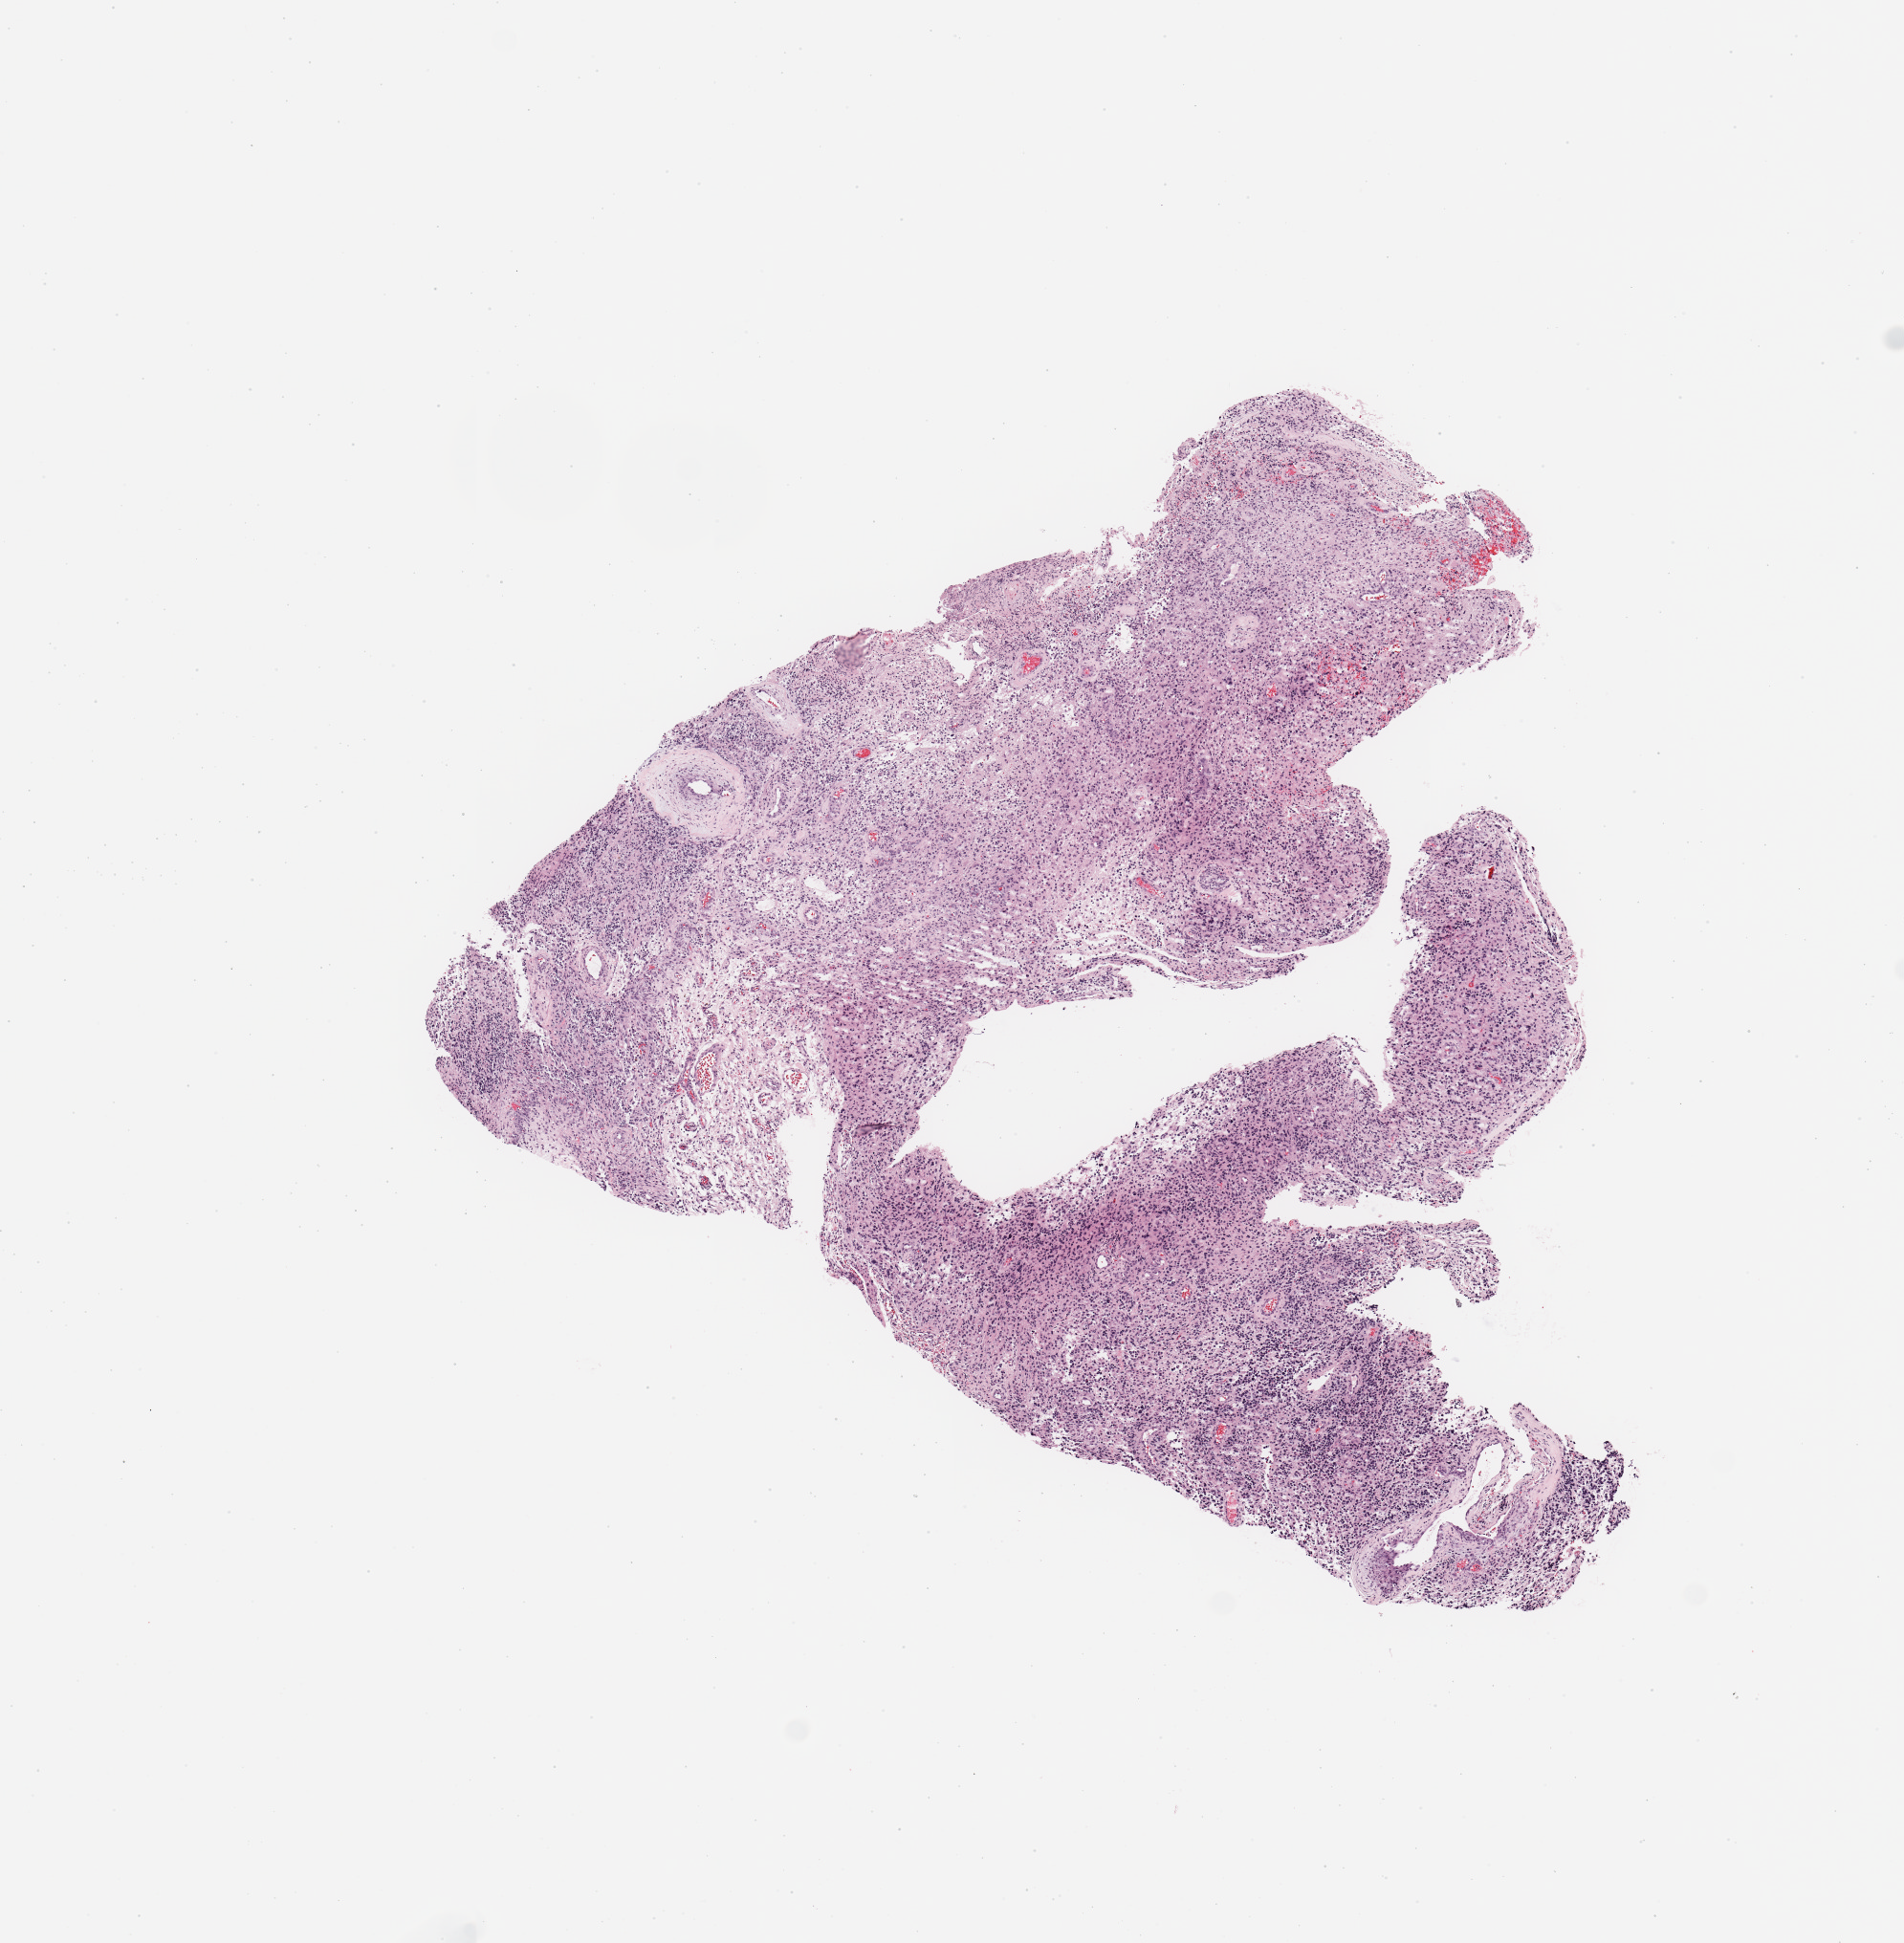
Whole-slide histology image, H&E, low-resolution overview of the scanned area, about 7.9 x 8.0 mm (acquisition: 20x scan). Brain, tumour tissue. 58-year-old female patient.
Histologic diagnosis: Glioblastoma.